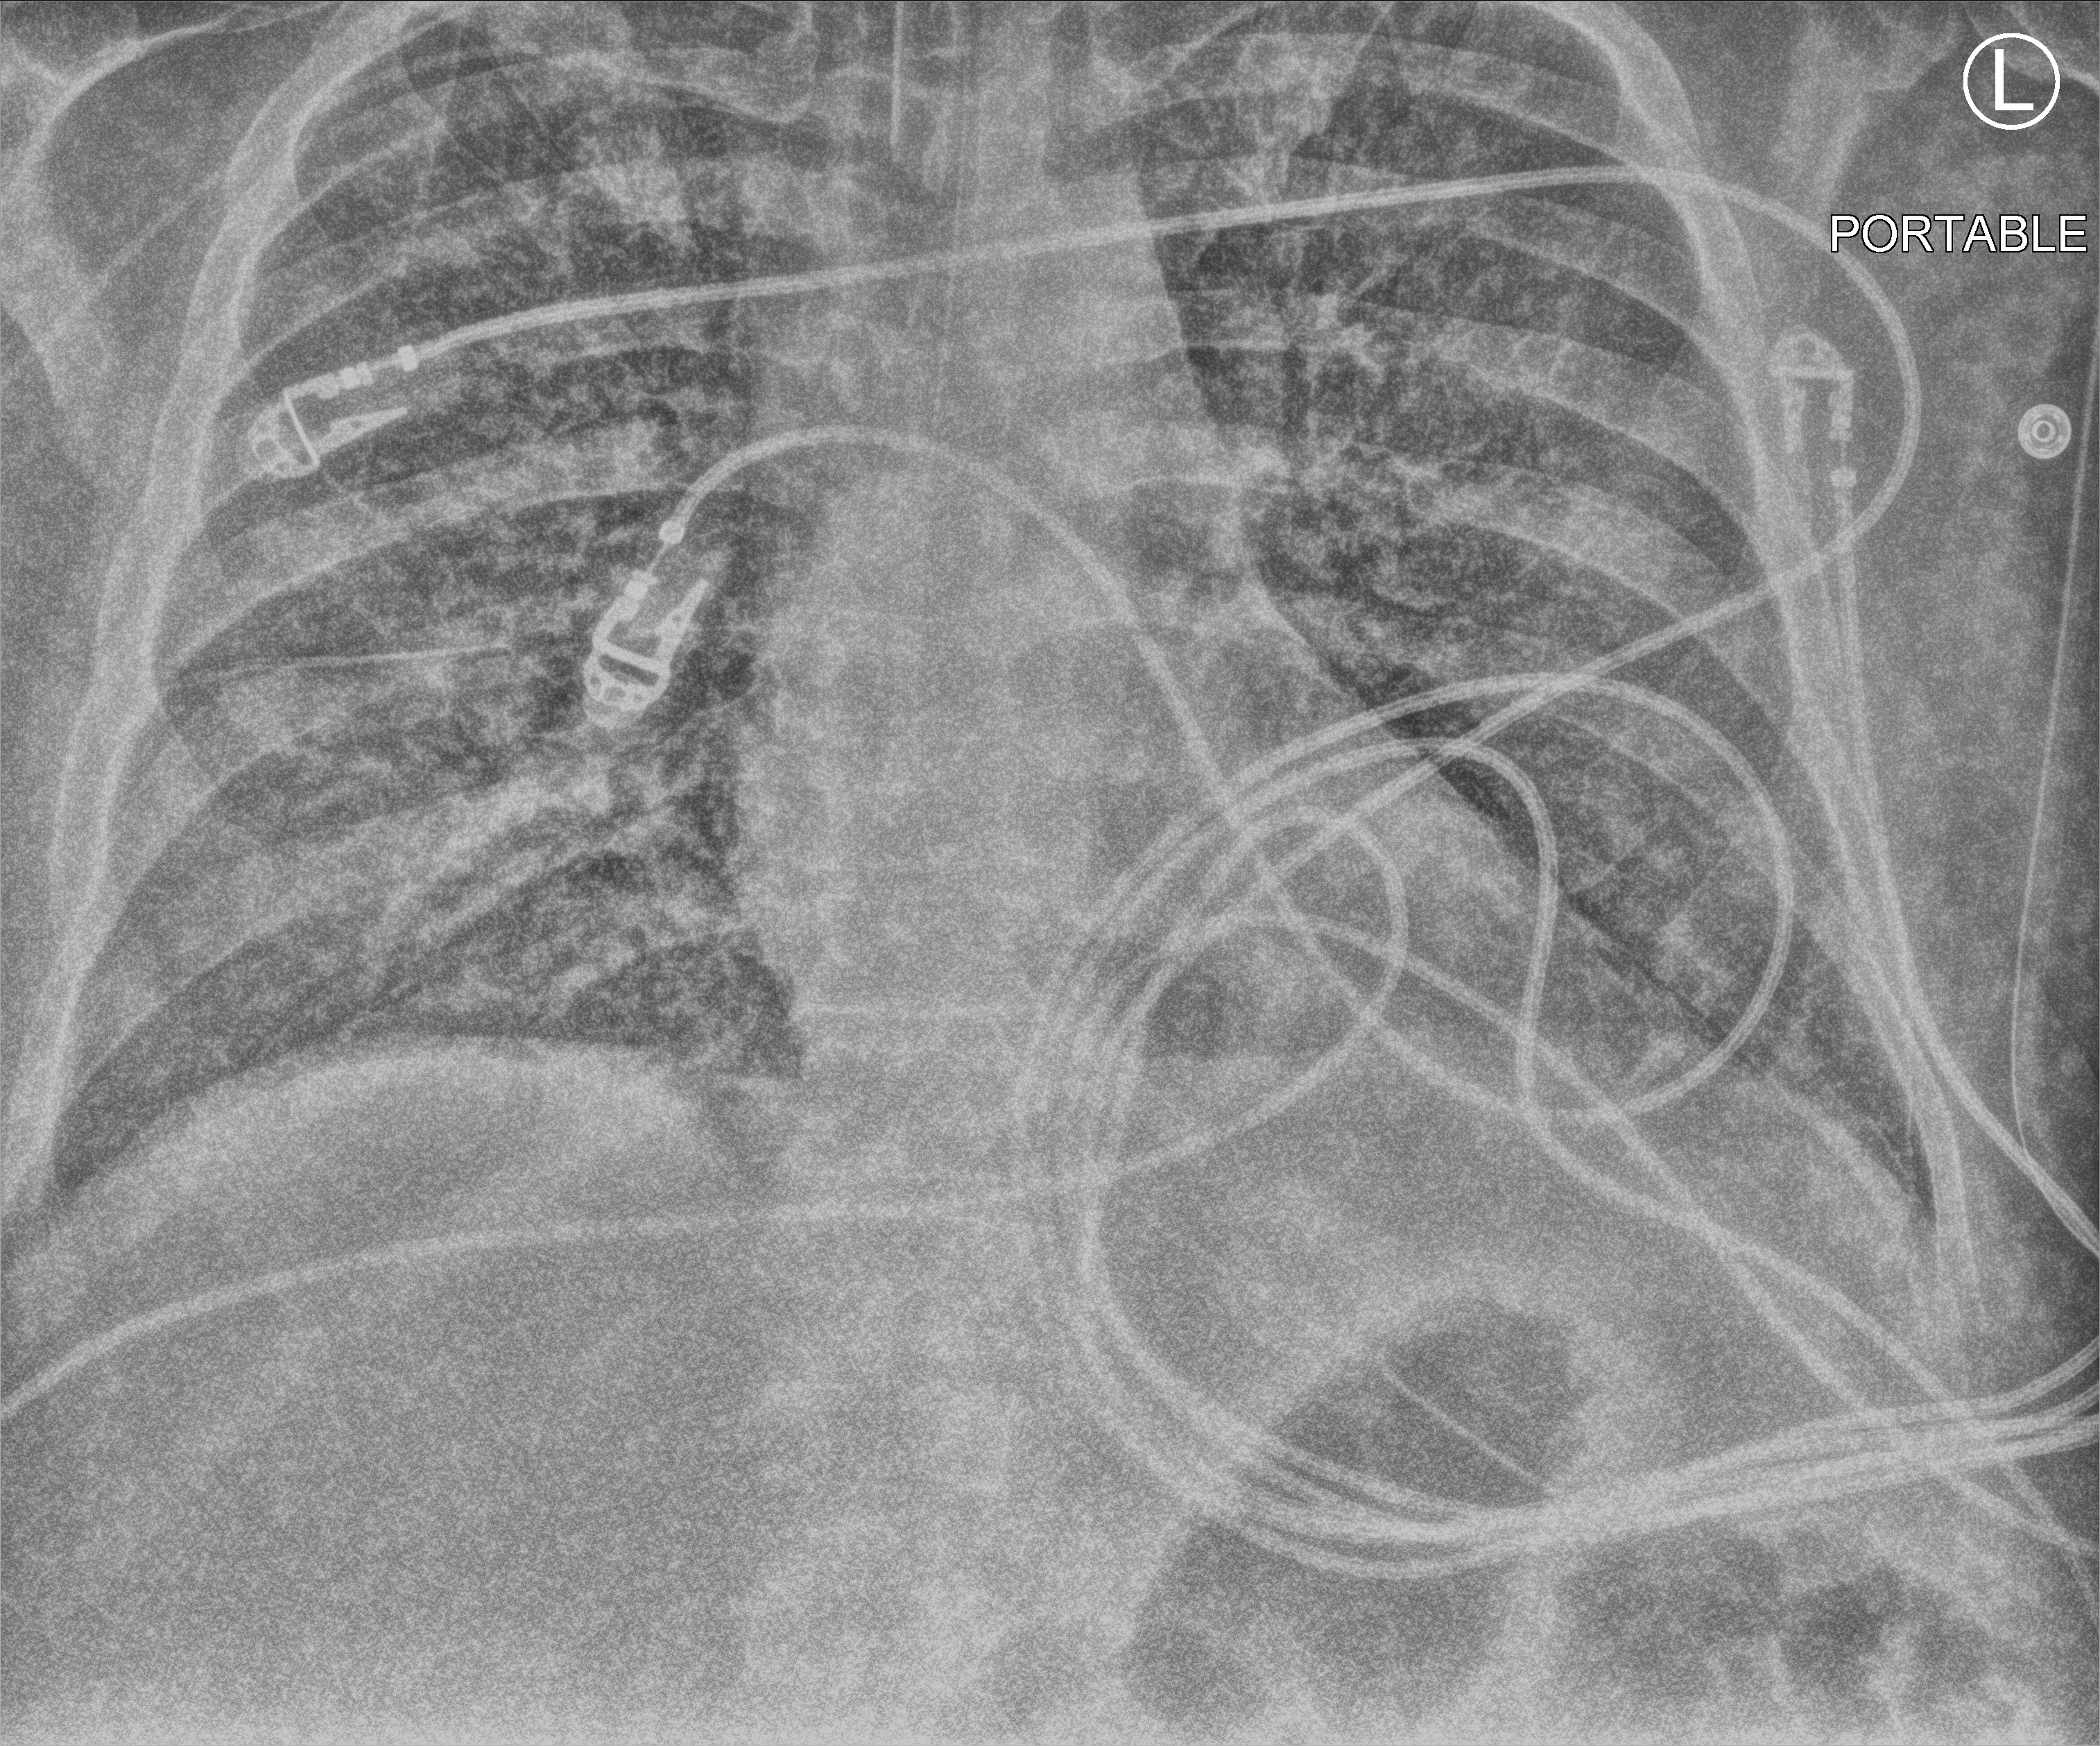
Chest X-ray (portable), anteroposterior (AP) projection. Patient hospitalised with COVID-19, aged 18–59 years.
Admission-level facts for this patient (not findings on this image; timing relative to this image not recorded): hypertension (admission record): yes; admitted to intensive care during this hospital stay: yes; mechanically ventilated during this hospital stay: yes.